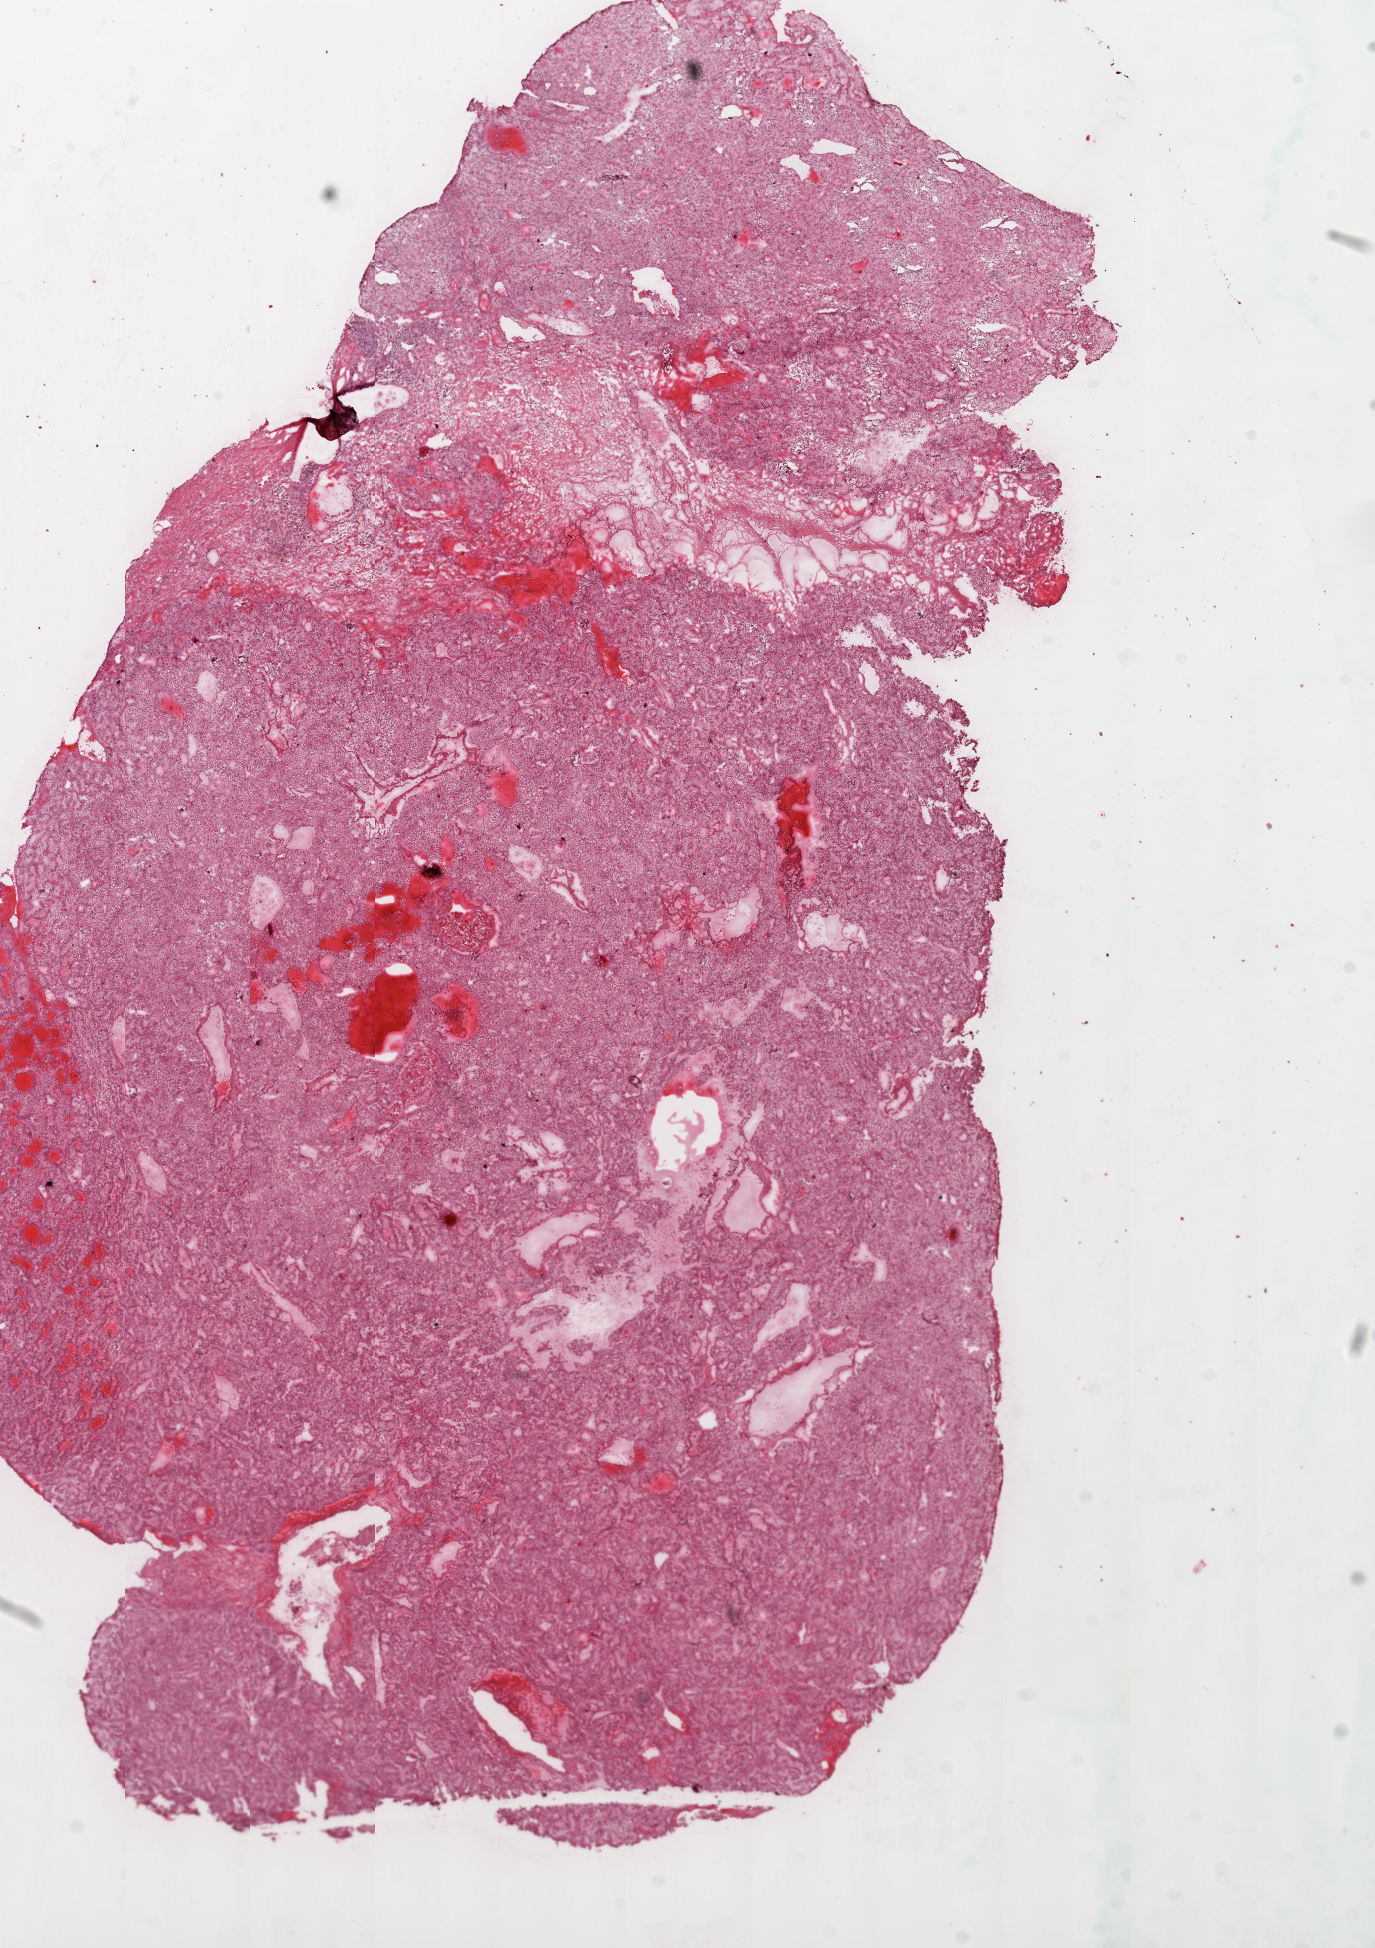
Digitized Hematoxylin and eosin (H&E) stained tissue section (whole slide) — shown as a low-resolution overview of the whole scanned area (about 11.0 x 15.6 mm). Frozen section. Sample: primary tumour, kidney. Patient: male, age at initial diagnosis 76 years. Histologic grade: G2 (moderately differentiated). Pathologist review of this section (percent, as recorded): tumour cells 90%, tumour nuclei 85%, normal cells 0%, stromal cells 10%, necrosis 0%.
AJCC pathologic stage: III. Diagnosis: Clear cell adenocarcinoma, NOS. Lymph nodes positive (case pathology): 0 of 5 examined.